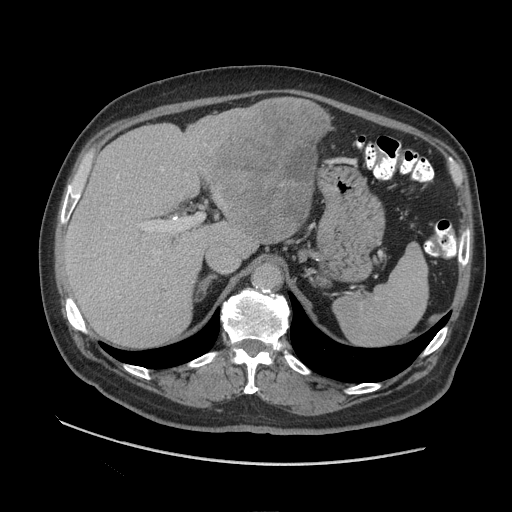
Contrast-enhanced abdominal CT (liver protocol), one axial slice; position 62 of 109 along the scan axis; reconstruction kernel STANDARD; soft-tissue window (W 400 / L 40 HU); 2.5 mm slice thickness; 512 × 512 image matrix, field of view 420 × 420 mm. Case-level facts recorded for this patient, not image findings: diagnosis: hepatocellular carcinoma (patient treated with transarterial chemoembolisation; whether this scan precedes or follows treatment is not stated here); TNM stage (as recorded): Stage-I; Child-Pugh class: A.
Annotated regions visible in this slice (semi-automatic segmentation, software-assisted and operator-edited):
- liver parenchyma outside the tumour (the mass and vessels are separate outlines, so this box may not span the whole liver): bounding box [x1, y1, x2, y2] px = [64, 100, 264, 346]
- mass: [198, 96, 332, 243]
- liver vessels: [117, 168, 169, 298]